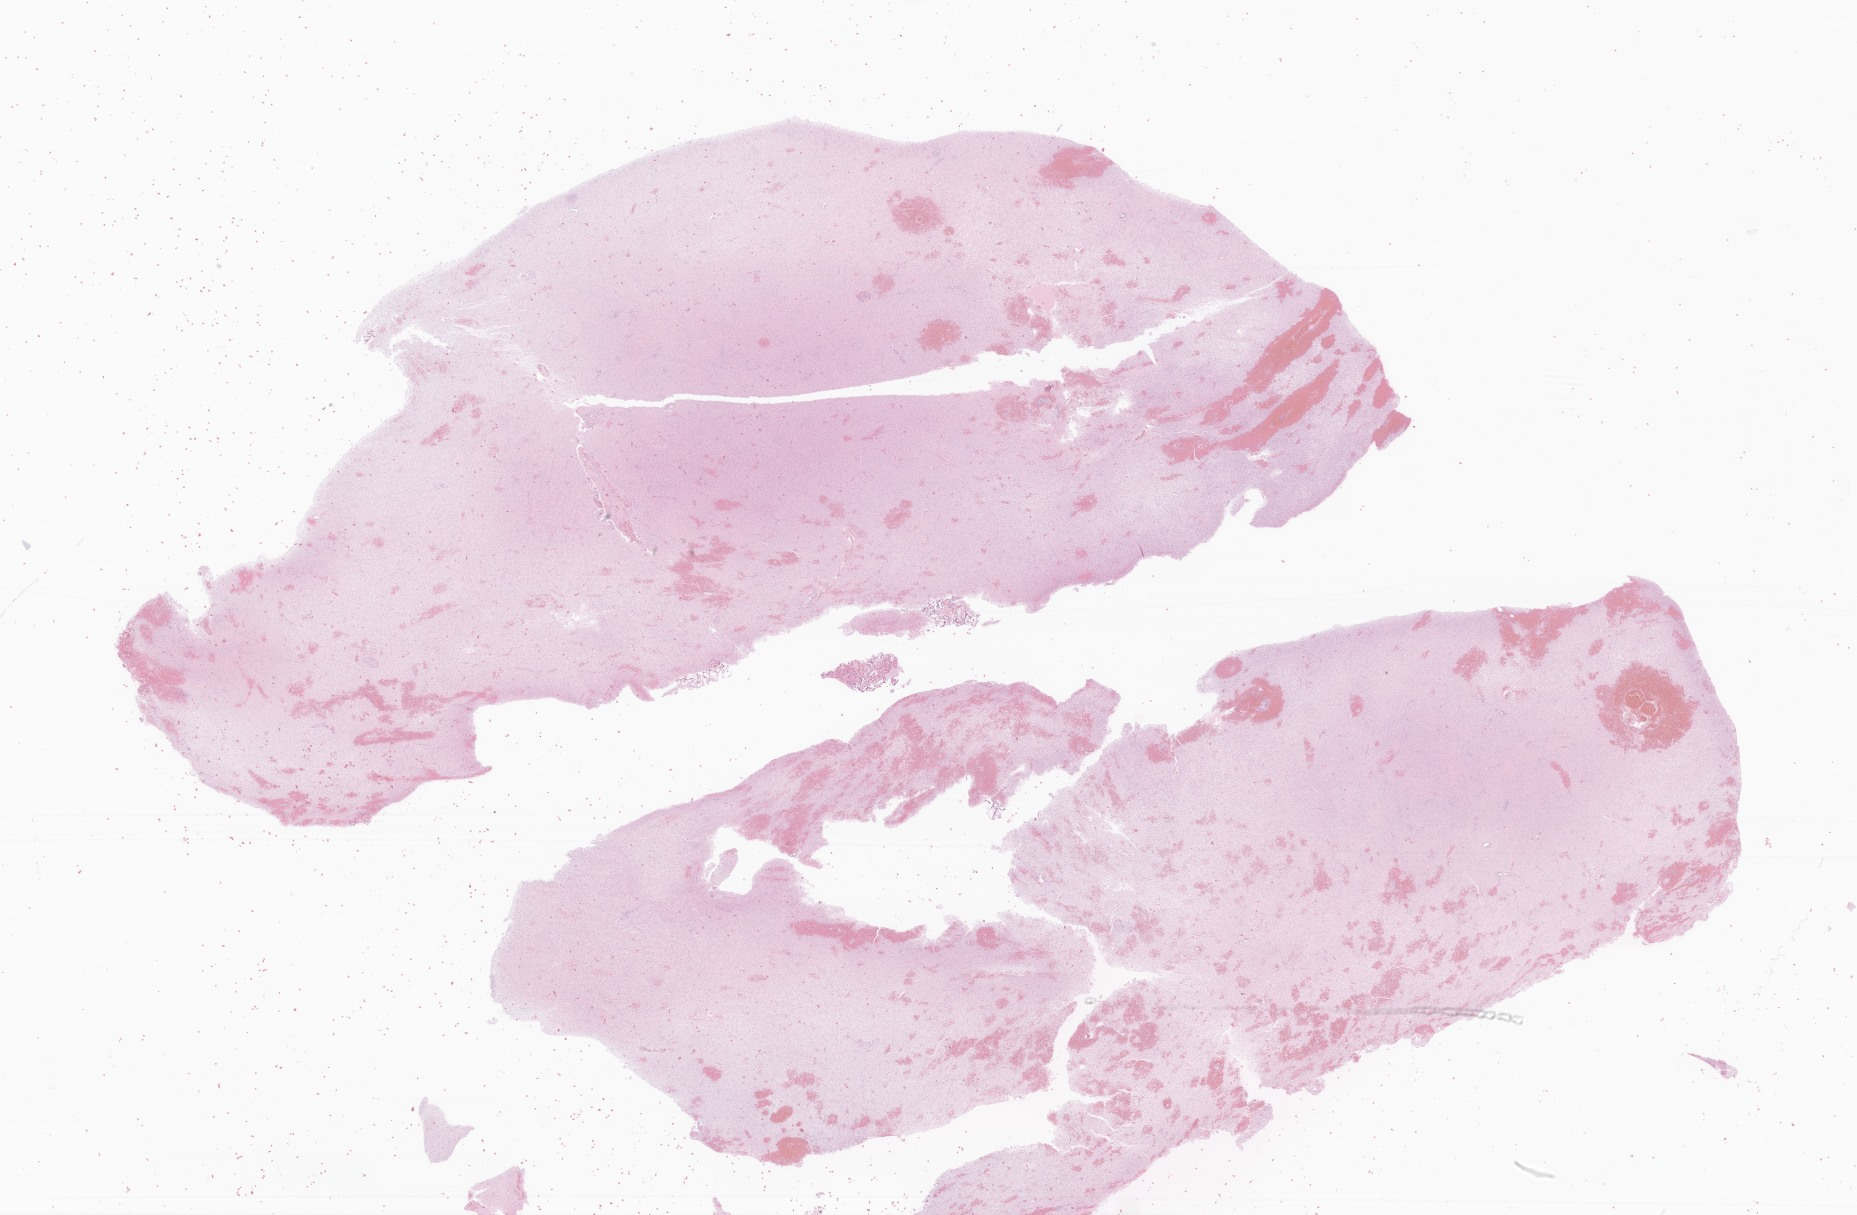
Digitized haematoxylin and eosin-stained section of tumor tissue from the brain — low-resolution overview of the scanned area, about 31.3 x 20.5 mm. Formalin-fixed, paraffin-embedded (FFPE) tissue. Patient: male, age 100 months (8 years 4 months).
• recorded diagnosis: Pilocytic astrocytoma